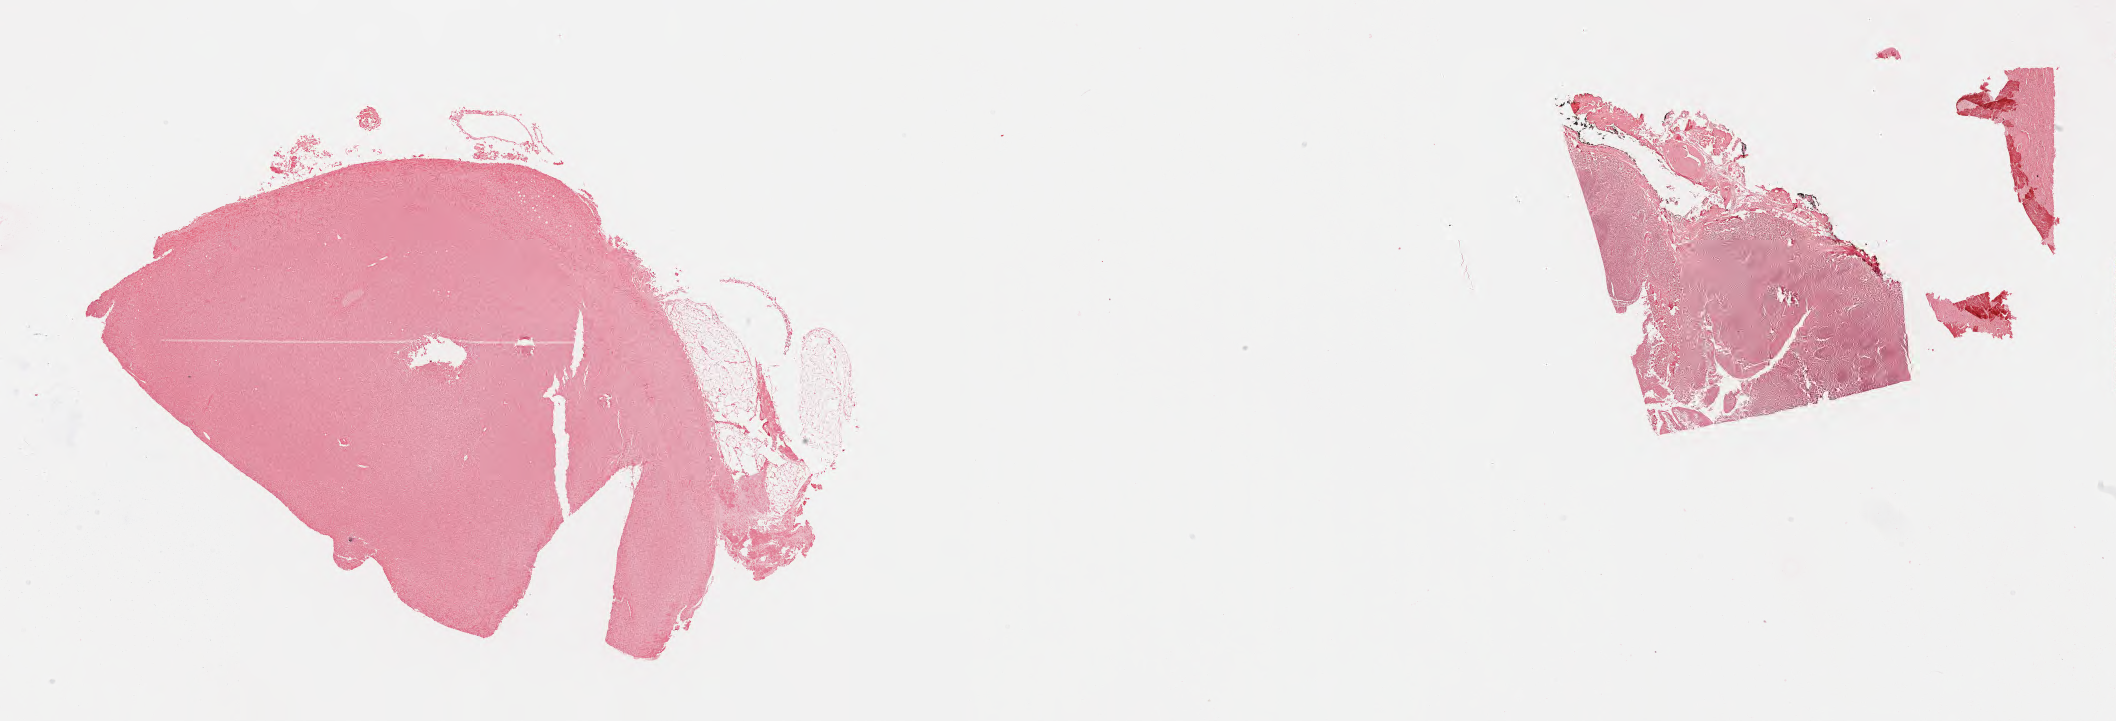
Whole-slide image, Epstein–Barr virus-encoded RNA (EBER) in-situ hybridisation — shown as a low-resolution overview of the whole scanned area (about 34.2 x 11.7 mm), tumor tissue, site: lymph node. Patient: male, aged 26.
Diagnosis: Diffuse large B-cell lymphoma, NOS.